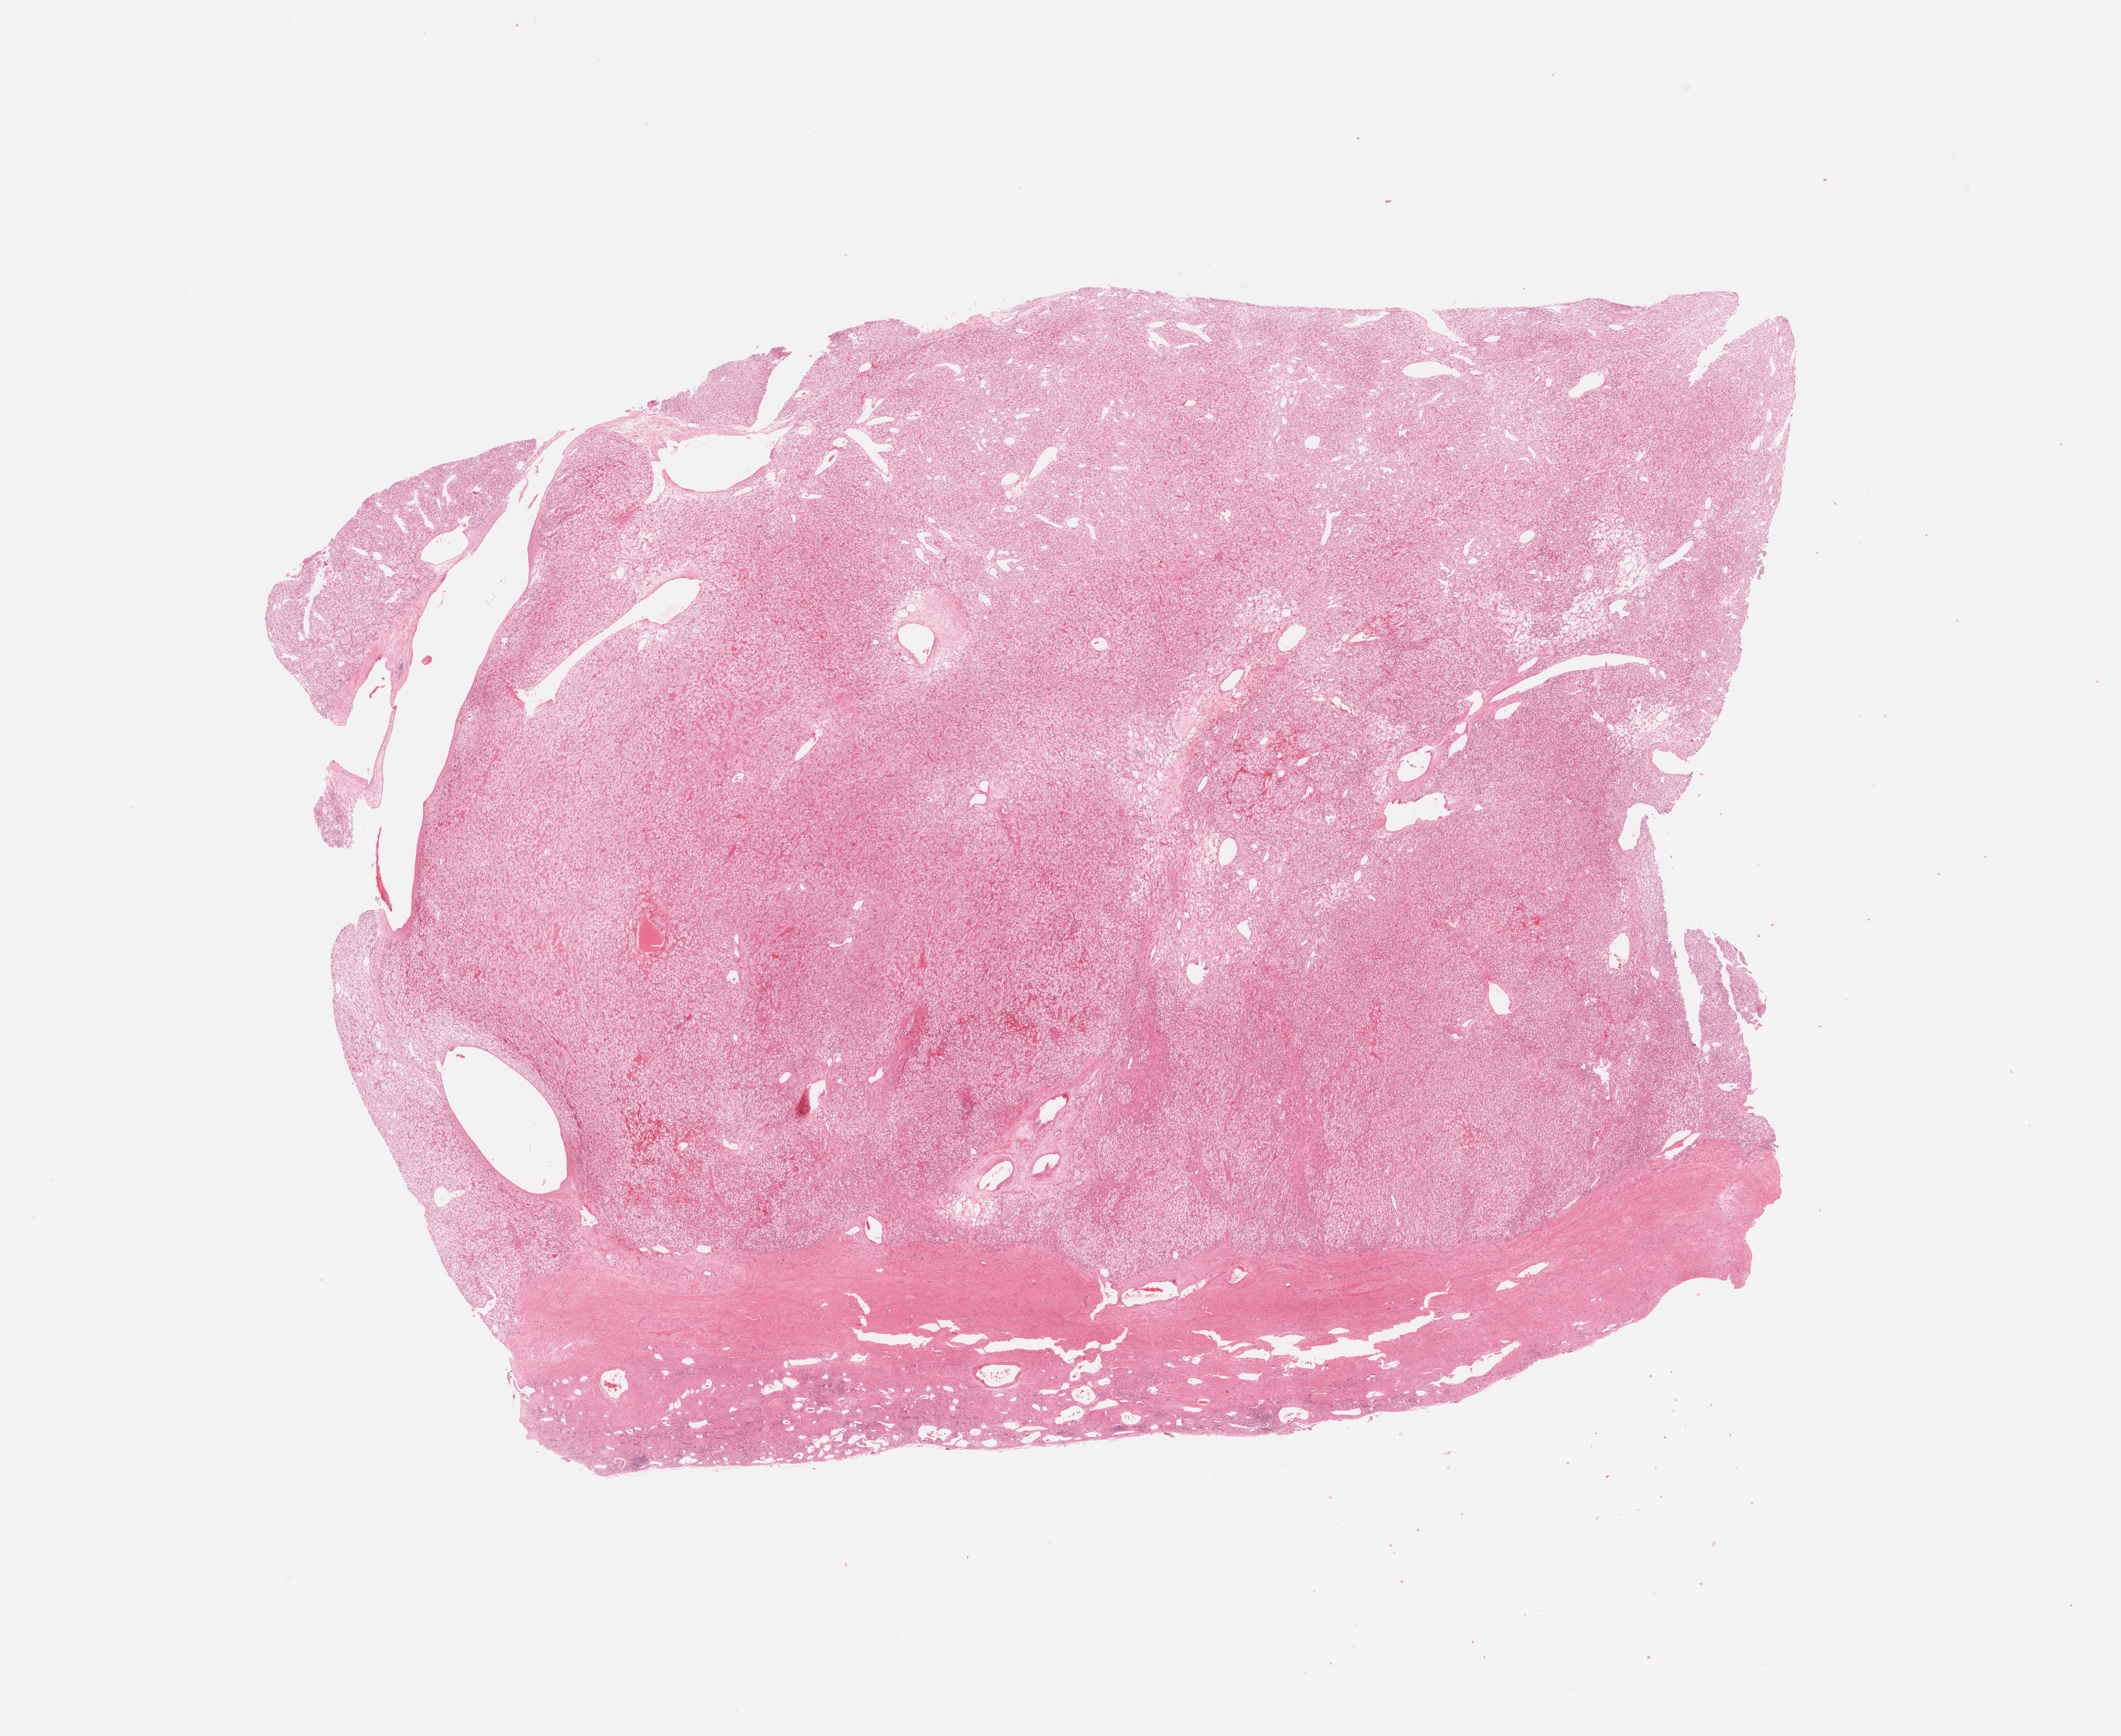
Digitized H&E-stained tissue section (whole slide) — shown as a low-resolution overview of the whole scanned area (about 21.7 x 17.7 mm, from a 20x scan), kidney, tumour tissue. 41-year-old female patient. Histologic grade: G2 (moderately differentiated).
Diagnosis: Renal cell carcinoma, NOS. Primary tumour site (as recorded): lower pole.